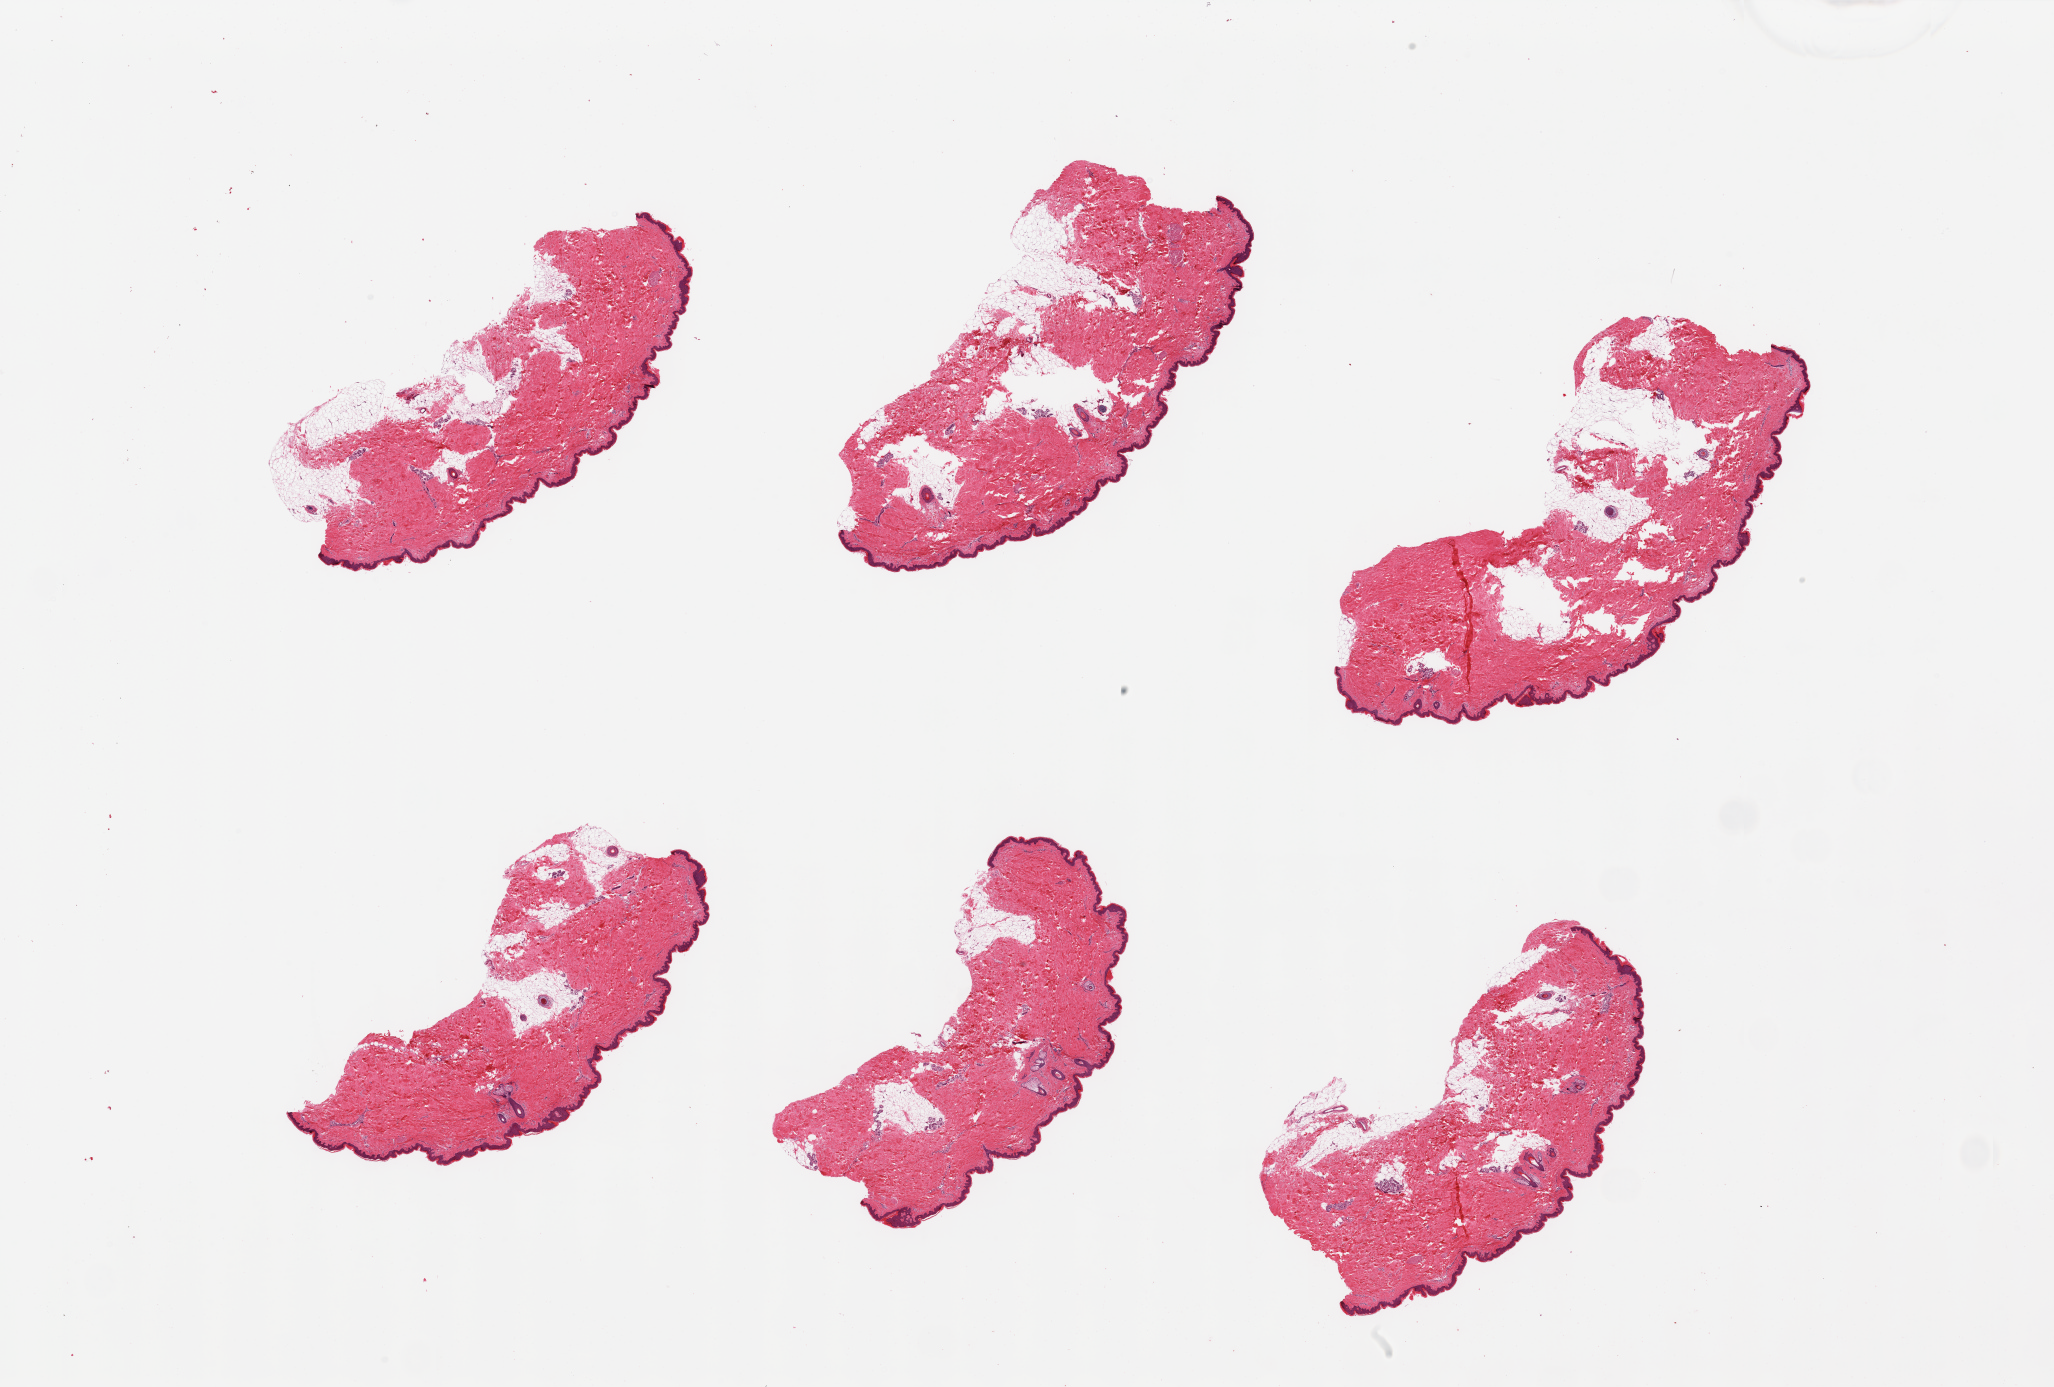
Whole-slide image, haematoxylin and eosin stain, whole scanned area (about 32.5 x 21.9 mm) shown as a low-resolution overview; PAXgene-fixed, paraffin-embedded tissue; section of skin of lower leg (target tissue); donor tissue sample. Donor: female.
* review note (as recorded): 6 pieces; includes 10-20% attached and internal fat, epidermis measures 42 microns